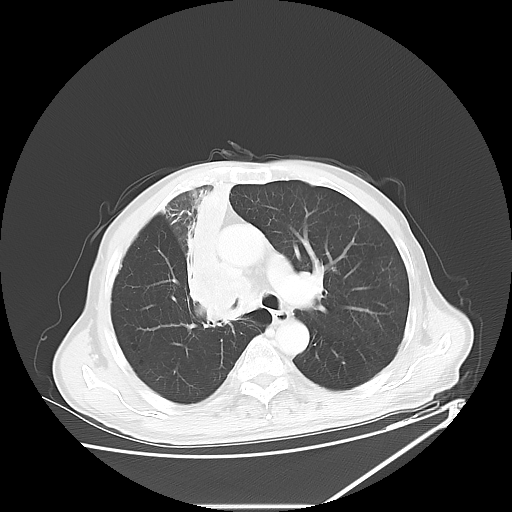
Chest CT, one axial slice; reconstruction kernel LUNG; 120 kVp; lung window (W 1500 / L -600 HU); 5 mm slice thickness; 512 × 512 image matrix, field of view 410 × 410 mm. Male patient, age 73 years. From the clinical record (not read from this slice): clinical TNM (as recorded): T2a N1 M0.
Outlined on this slice (rectangle marked by the reading radiologist):
- lung tumour (recorded histology: squamous cell carcinoma): bounding box <169,176,254,340> (left, top, right, bottom; pixels)